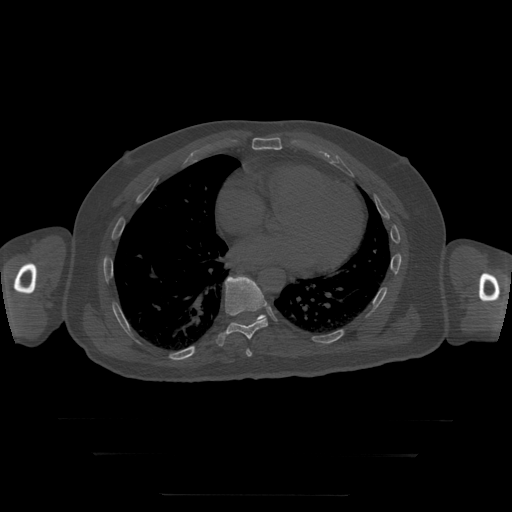
CT including the spine, one axial slice; position 142 of 397 along the scan axis; reconstruction kernel STANDARD; 120 kVp; bone window (W 1800 / L 400 HU); 512 × 512 image matrix. Patient age 73 years. Case-level facts recorded for this patient, not image findings: primary cancer: prostate.
Annotated regions visible in this slice (semi-automatically segmented with operator editing):
- T10 vertebra: box from (x=233, y=315) to (x=266, y=324) px
- T8 vertebra: (x=246, y=349)–(x=252, y=357)
- T9 vertebra: (x=216, y=277)–(x=268, y=346)